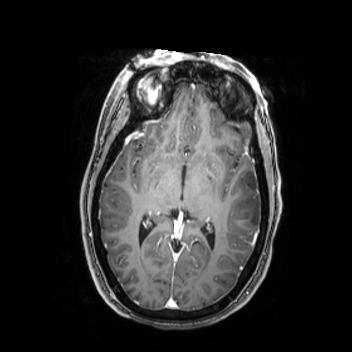
Brain MRI from a brain-tumour surgery series, one axial slice. Slice 147 of 350 in the series (ordered by position). T1-weighted post-contrast. 0.9 mm slice thickness. 352 × 352 image matrix, field of view 280 × 280 mm. From the clinical record (not read from this slice): histopathology: Oligodendroglioma; WHO grade: 2.
Structures marked on this image (outlined manually by an expert reader):
- tumour: box from (x=224, y=175) to (x=262, y=227) px